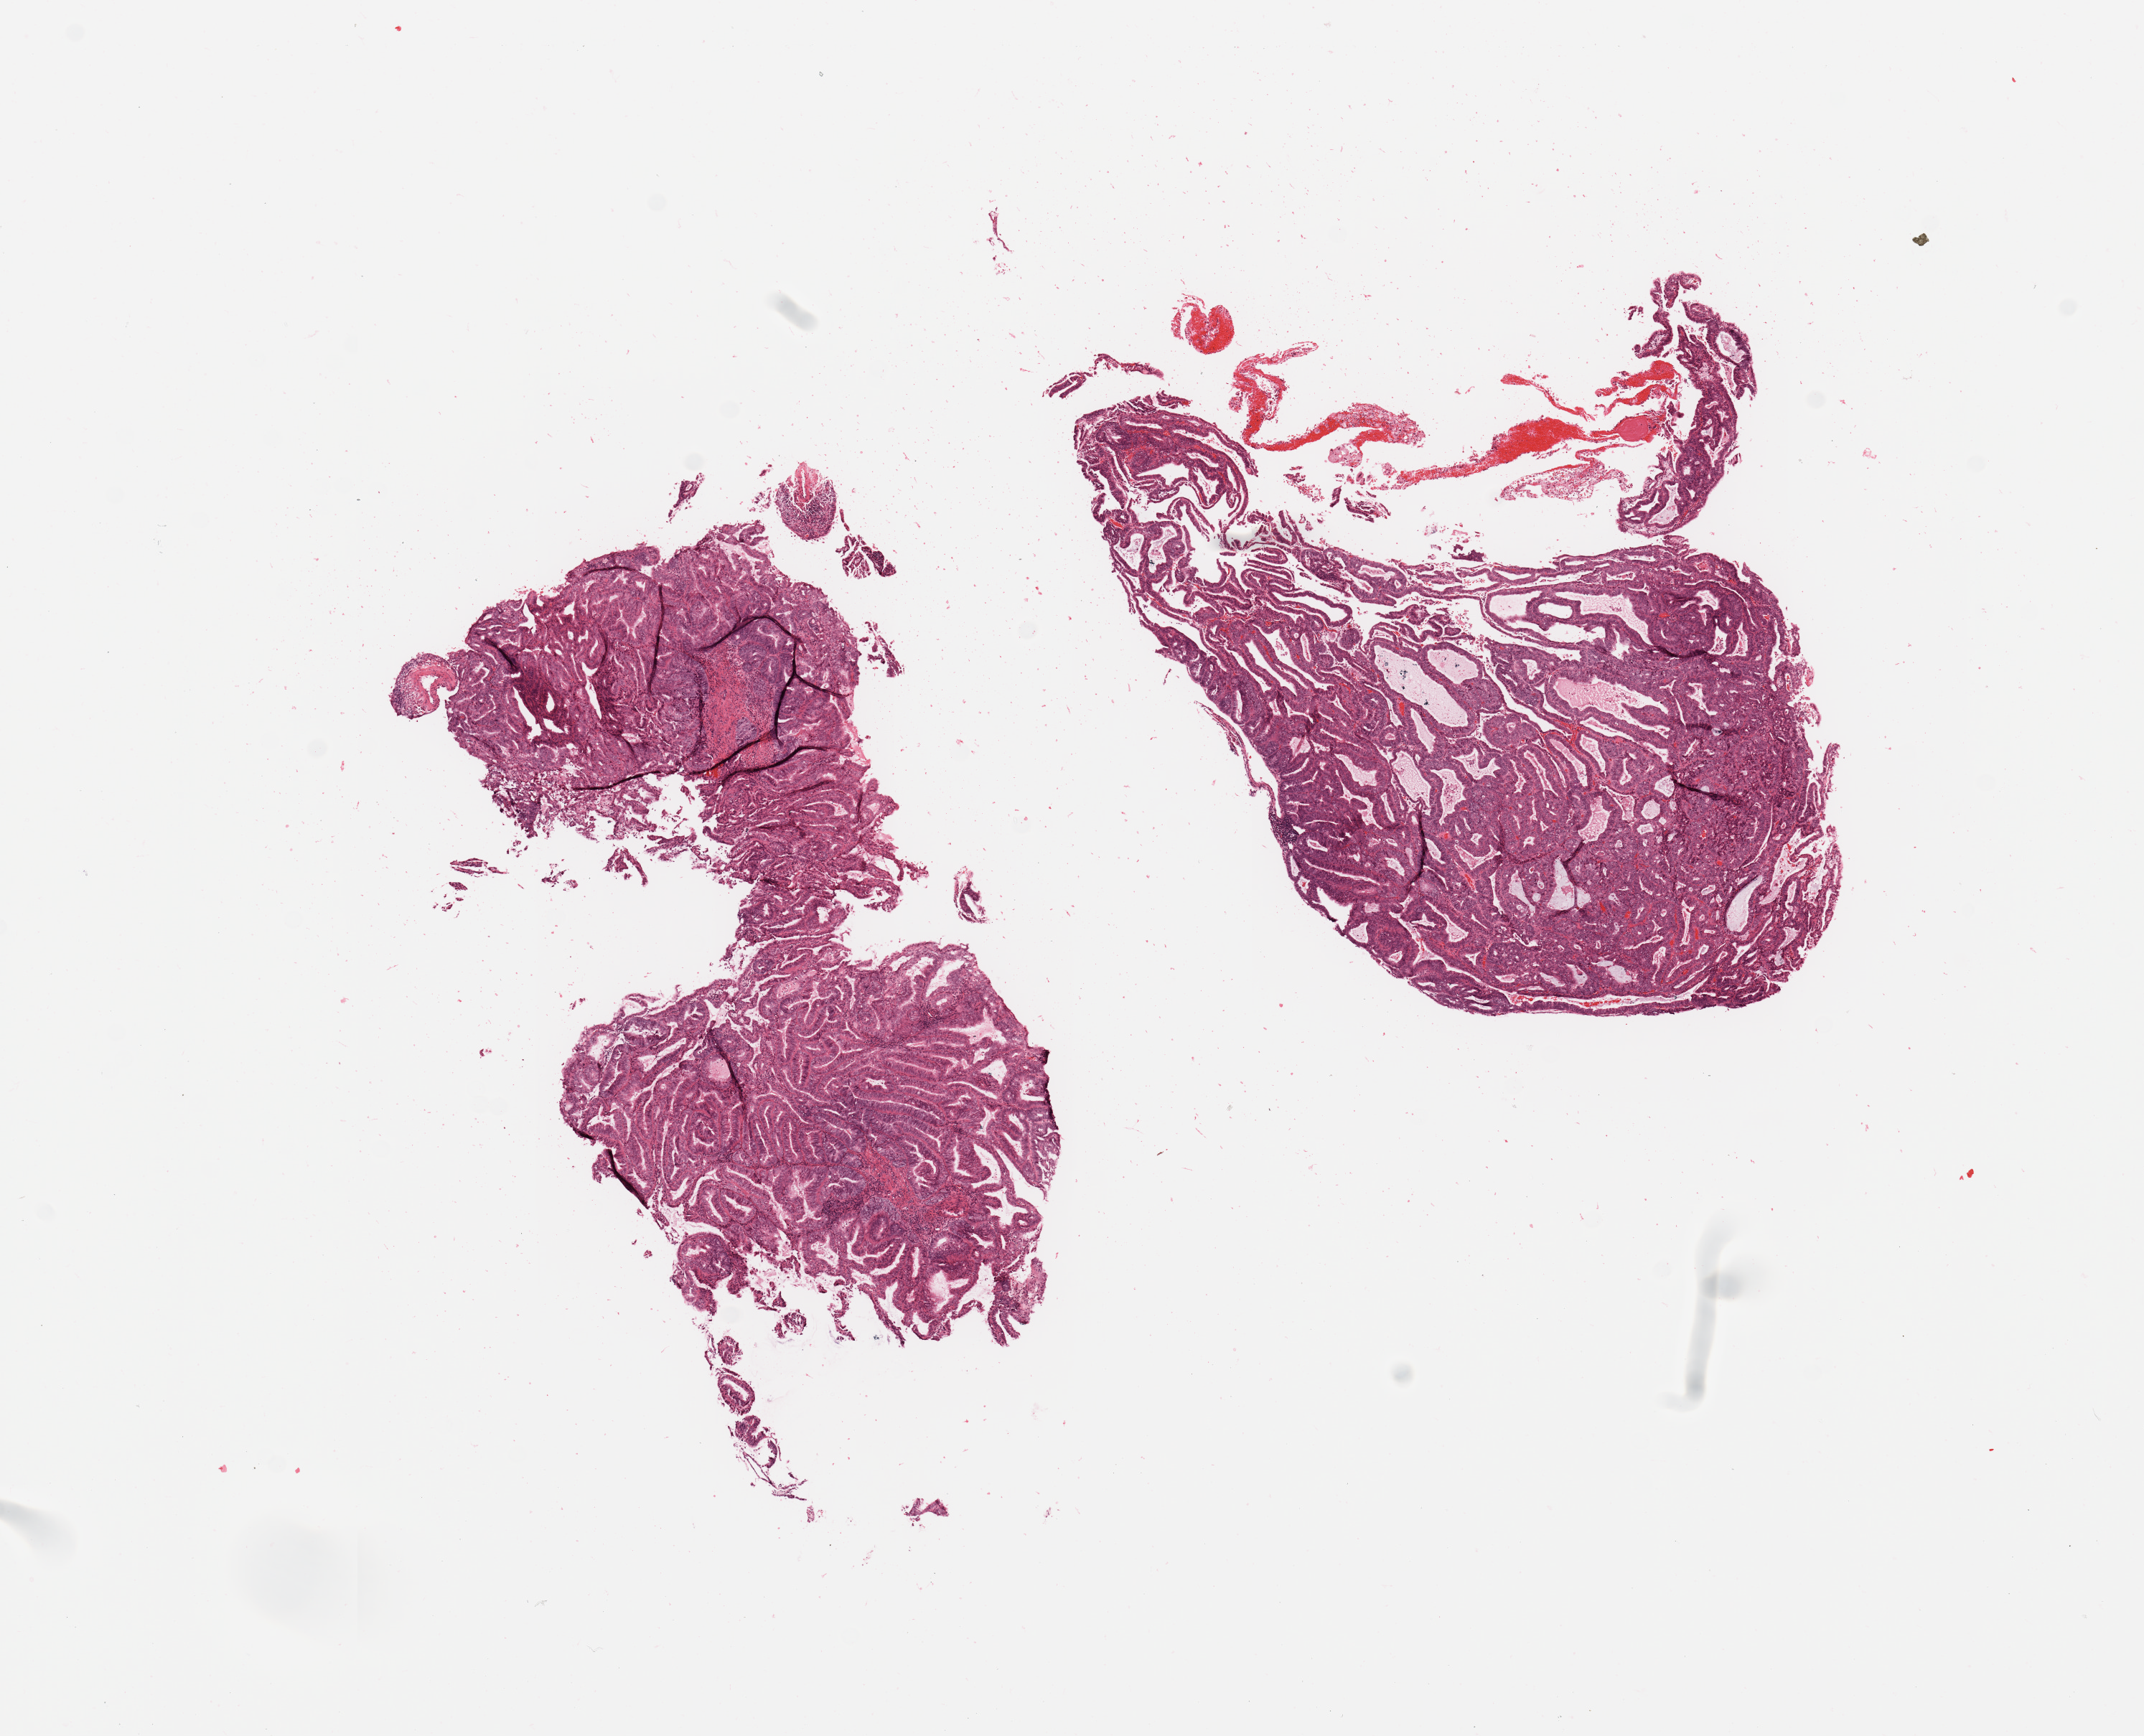
Hematoxylin and eosin (H&E) stained whole-slide image, whole scanned area (about 11.8 x 9.6 mm) shown as a low-resolution overview; uterus, tumour tissue. 74-year-old female patient. Histologic grade: G1 (well differentiated).
* diagnosis: Endometrioid adenocarcinoma, NOS
* AJCC pathologic stage: I